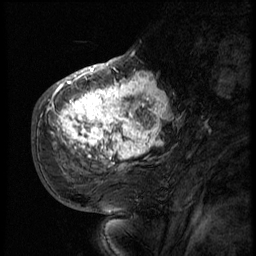
Breast MRI (dynamic contrast-enhanced), one sagittal slice. 3 images stored at this slice position (order not interpretable as contrast timing). 1.5 T. TE 4.2 ms, TR 9 ms. 256 × 256 image matrix. Female patient, age 51 years. Case-level facts recorded for this patient, not image findings: setting: breast cancer imaged before/during neoadjuvant chemotherapy; receptor status: triple-negative.
Structures marked on this image (semi-automatic segmentation, software-assisted and operator-edited):
- analysis volume of interest (the breast-tissue region the enhancement analysis was run in; not a lesion): box from (x=52, y=66) to (x=174, y=179) px
- tumour enhancement mask (voxels above the 140 % enhancement threshold inside the analysis volume of interest): (x=52, y=66)–(x=170, y=161)